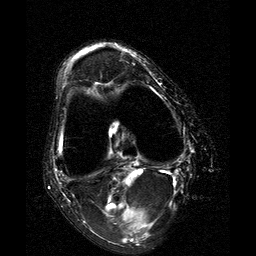
MRI of an extremity soft-tissue mass, one axial slice. Position 6 of 25 along the scan axis. T2-weighted fat-saturated. 256 × 256 image matrix, field of view 160 × 160 mm. Female patient. From the clinical record (not read from this slice): histological type: liposarcoma; site of the primary tumour: right thigh.
Structures marked on this image (expert manual segmentation):
- gross tumour volume (mass): bounding box <115,208,146,236> (left, top, right, bottom; pixels)